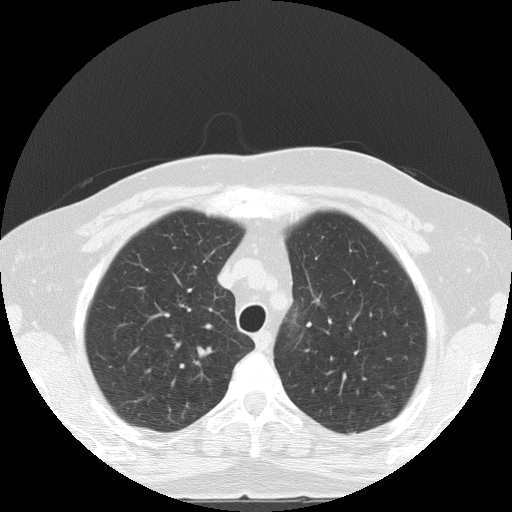
Low-dose screening chest CT, one axial slice. Position 106 of 133 along the scan axis. 120 kVp. Lung window (W 1500 / L -600 HU). 2 mm slice thickness. 512 × 512 image matrix.
Outlined on this slice (outlined manually by an expert reader):
- lesion 1 (tumor, upper lobe of right lung): box from (x=199, y=354) to (x=208, y=355) px